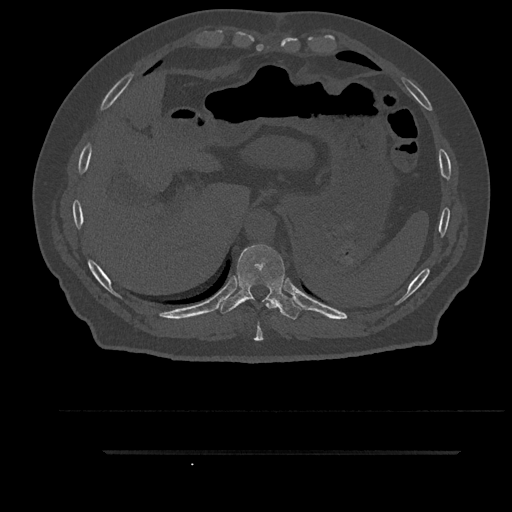
CT including the spine, one axial slice; bone window (W 1800 / L 400 HU); 0.5 mm slice thickness; 512 × 512 image matrix. Male patient, age 63 years. From the clinical record (not read from this slice): primary cancer: renal.
Structures marked on this image (semi-automatically segmented with operator editing):
- T10 vertebra: bounding box (x1, y1, x2, y2) in pixels: (219, 244, 303, 319)
- T9 vertebra: (254, 299, 276, 341)